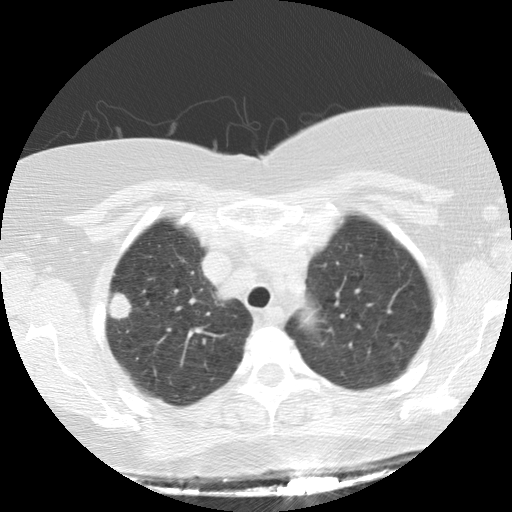
Low-dose screening chest CT, one axial slice; position 111 of 136 along the scan axis; reconstruction kernel STANDARD; 120 kVp; lung window (W 1500 / L -600 HU); 2.5 mm slice thickness; 512 × 512 image matrix.
Annotated regions visible in this slice (expert manual segmentation):
- lesion 1 (tumor, upper lobe of right lung): bounding box (x1, y1, x2, y2) in pixels: (109, 293, 131, 320)